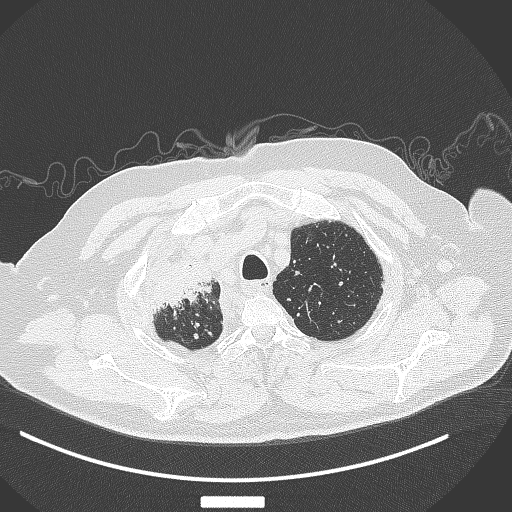
Chest CT, one axial slice. Position 316 of 384 along the scan axis. Reconstruction kernel B70f. 120 kVp. Lung window (W 1500 / L -600 HU). 512 × 512 image matrix. Patient: male, 69 years. Case-level facts recorded for this patient, not image findings: clinical TNM (as recorded): T4 N3 M1.
Structures marked on this image (rectangle marked by the reading radiologist):
- lung tumour (recorded histology: adenocarcinoma): bounding box [x1, y1, x2, y2] px = [151, 257, 222, 321]